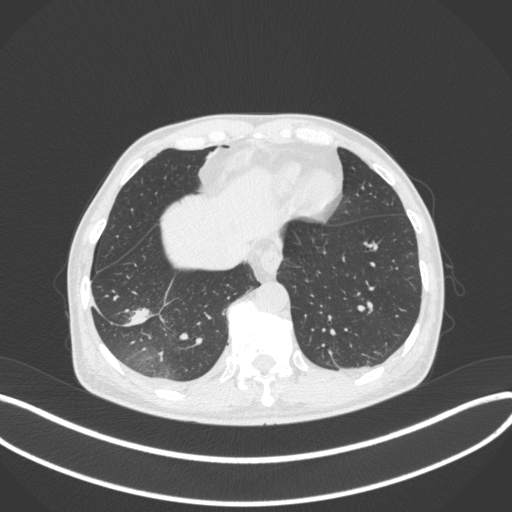
Chest CT, one axial slice. Position 86 of 385 along the scan axis. Reconstruction kernel B31f. Lung window (W 1500 / L -600 HU). 1 mm slice thickness. 512 × 512 image matrix. Male patient, age 64 years. Case-level facts recorded for this patient, not image findings: clinical TNM (as recorded): T3 N0 M0; histopathological grade: G2-3.
Annotated regions visible in this slice (rectangle marked by the reading radiologist):
- lung tumour (recorded histology: adenocarcinoma): bounding box <114,300,158,332> (left, top, right, bottom; pixels)